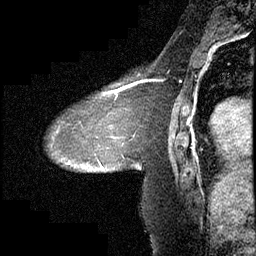
Breast MRI (dynamic contrast-enhanced), one sagittal slice. Slice 139 of 232 in the series (ordered by position). Dynamic contrast-enhanced study with each time point stored as its own series, time point 2 of 4 at this slice position (early post-contrast, ordered by acquisition time). 1.5 T. TE 4.2 ms, TR 6.7 ms. 3 mm slice thickness. 256 × 256 image matrix. Patient: female, 63 years. Case-level facts recorded for this patient, not image findings: setting: breast cancer imaged before/during neoadjuvant chemotherapy; receptor status: triple-negative.
Outlined on this slice (semi-automatic segmentation, software-assisted and operator-edited):
- analysis volume of interest (the breast-tissue region the enhancement analysis was run in; not a lesion): bounding box [x1, y1, x2, y2] px = [47, 90, 140, 173]
- tumour enhancement mask (voxels above the 70 % enhancement threshold inside the analysis volume of interest): [97, 90, 135, 168]